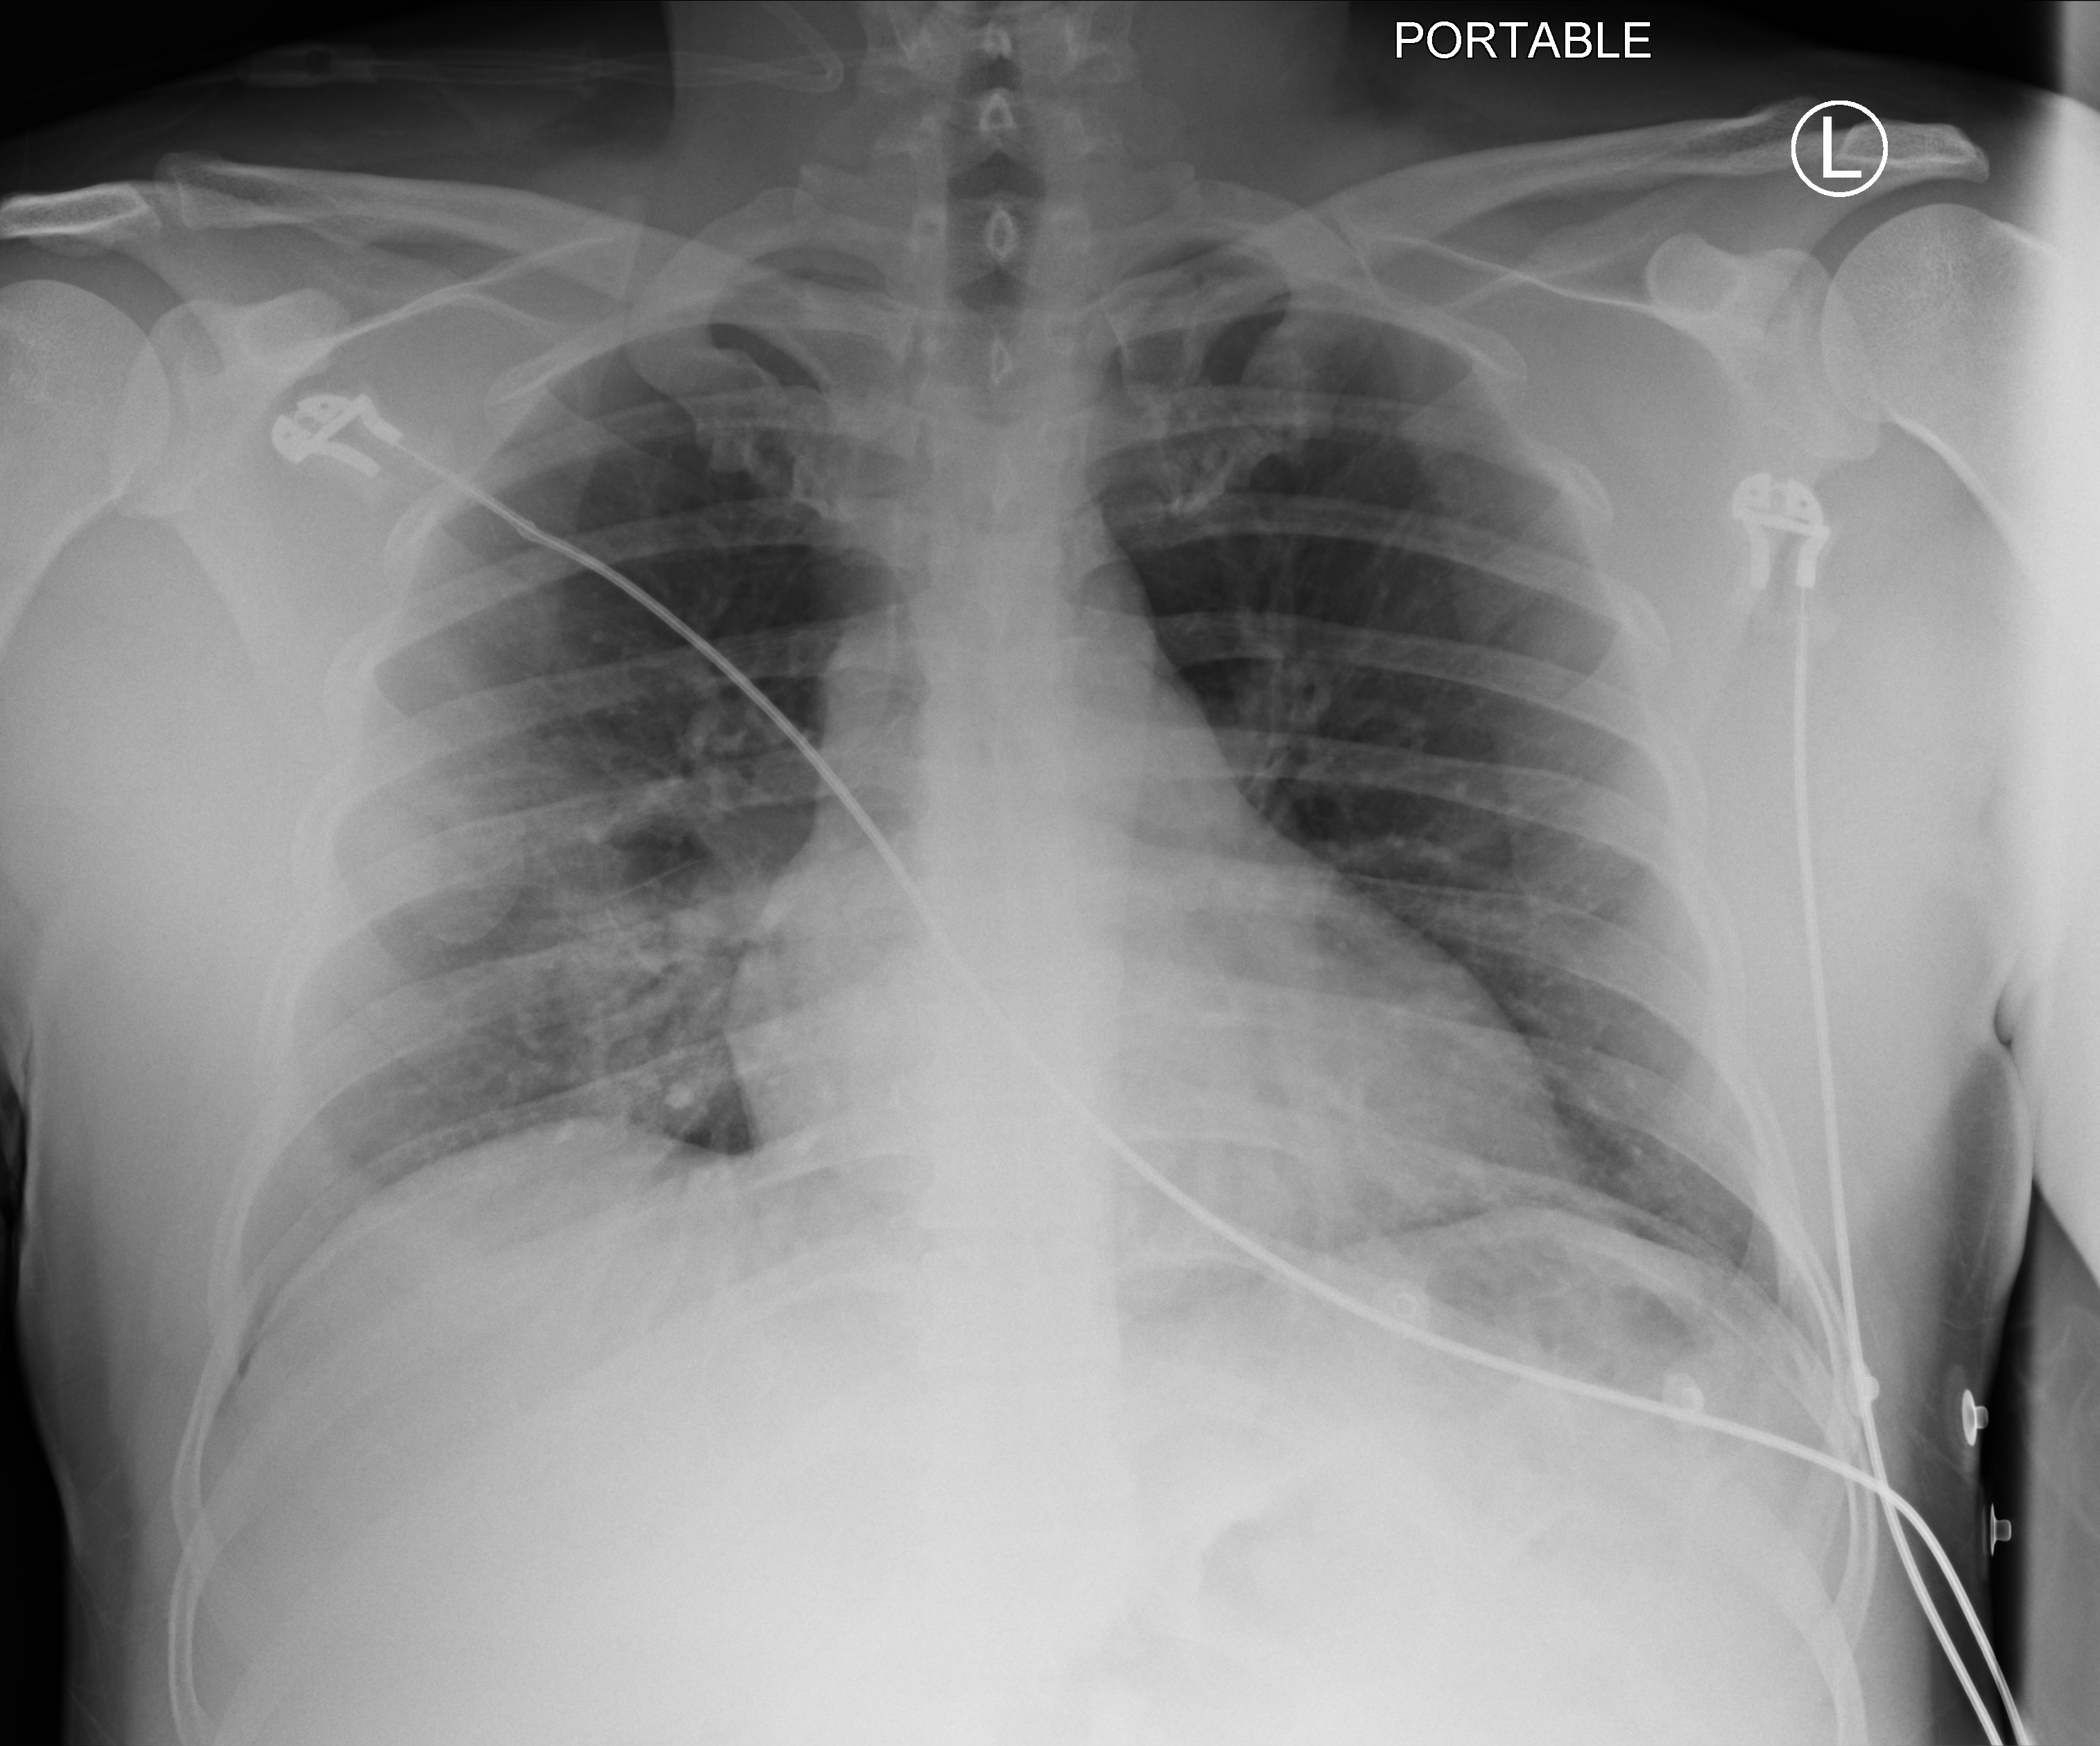
Portable chest radiograph; anteroposterior (AP) projection. Male patient hospitalised with COVID-19, age 18–59 years.
Hospital-stay facts (about this admission, not read from this image; timing relative to this image not recorded): smoking status (admission record): never; mechanically ventilated during this hospital stay: no; hypertension (admission record): yes.